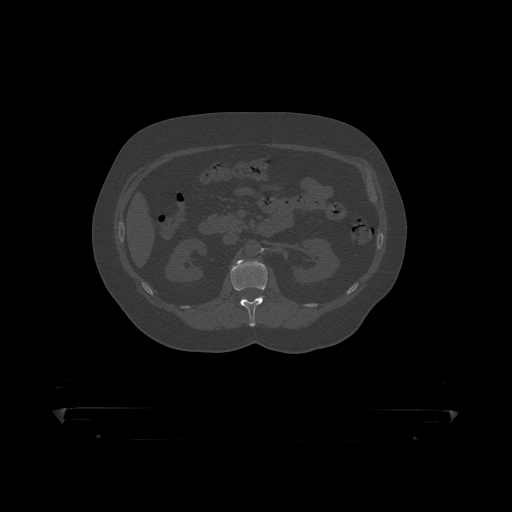
CT including the spine, one axial slice. Position 139 of 390 along the scan axis. Bone window (W 1800 / L 400 HU). 1.25 mm slice thickness. 512 × 512 image matrix. Male patient, age 60 years. Case-level facts recorded for this patient, not image findings: primary cancer: prostate.
Annotated regions visible in this slice (semi-automatic segmentation, software-assisted and operator-edited):
- L1 vertebra: bounding box <231,260,268,319> (left, top, right, bottom; pixels)